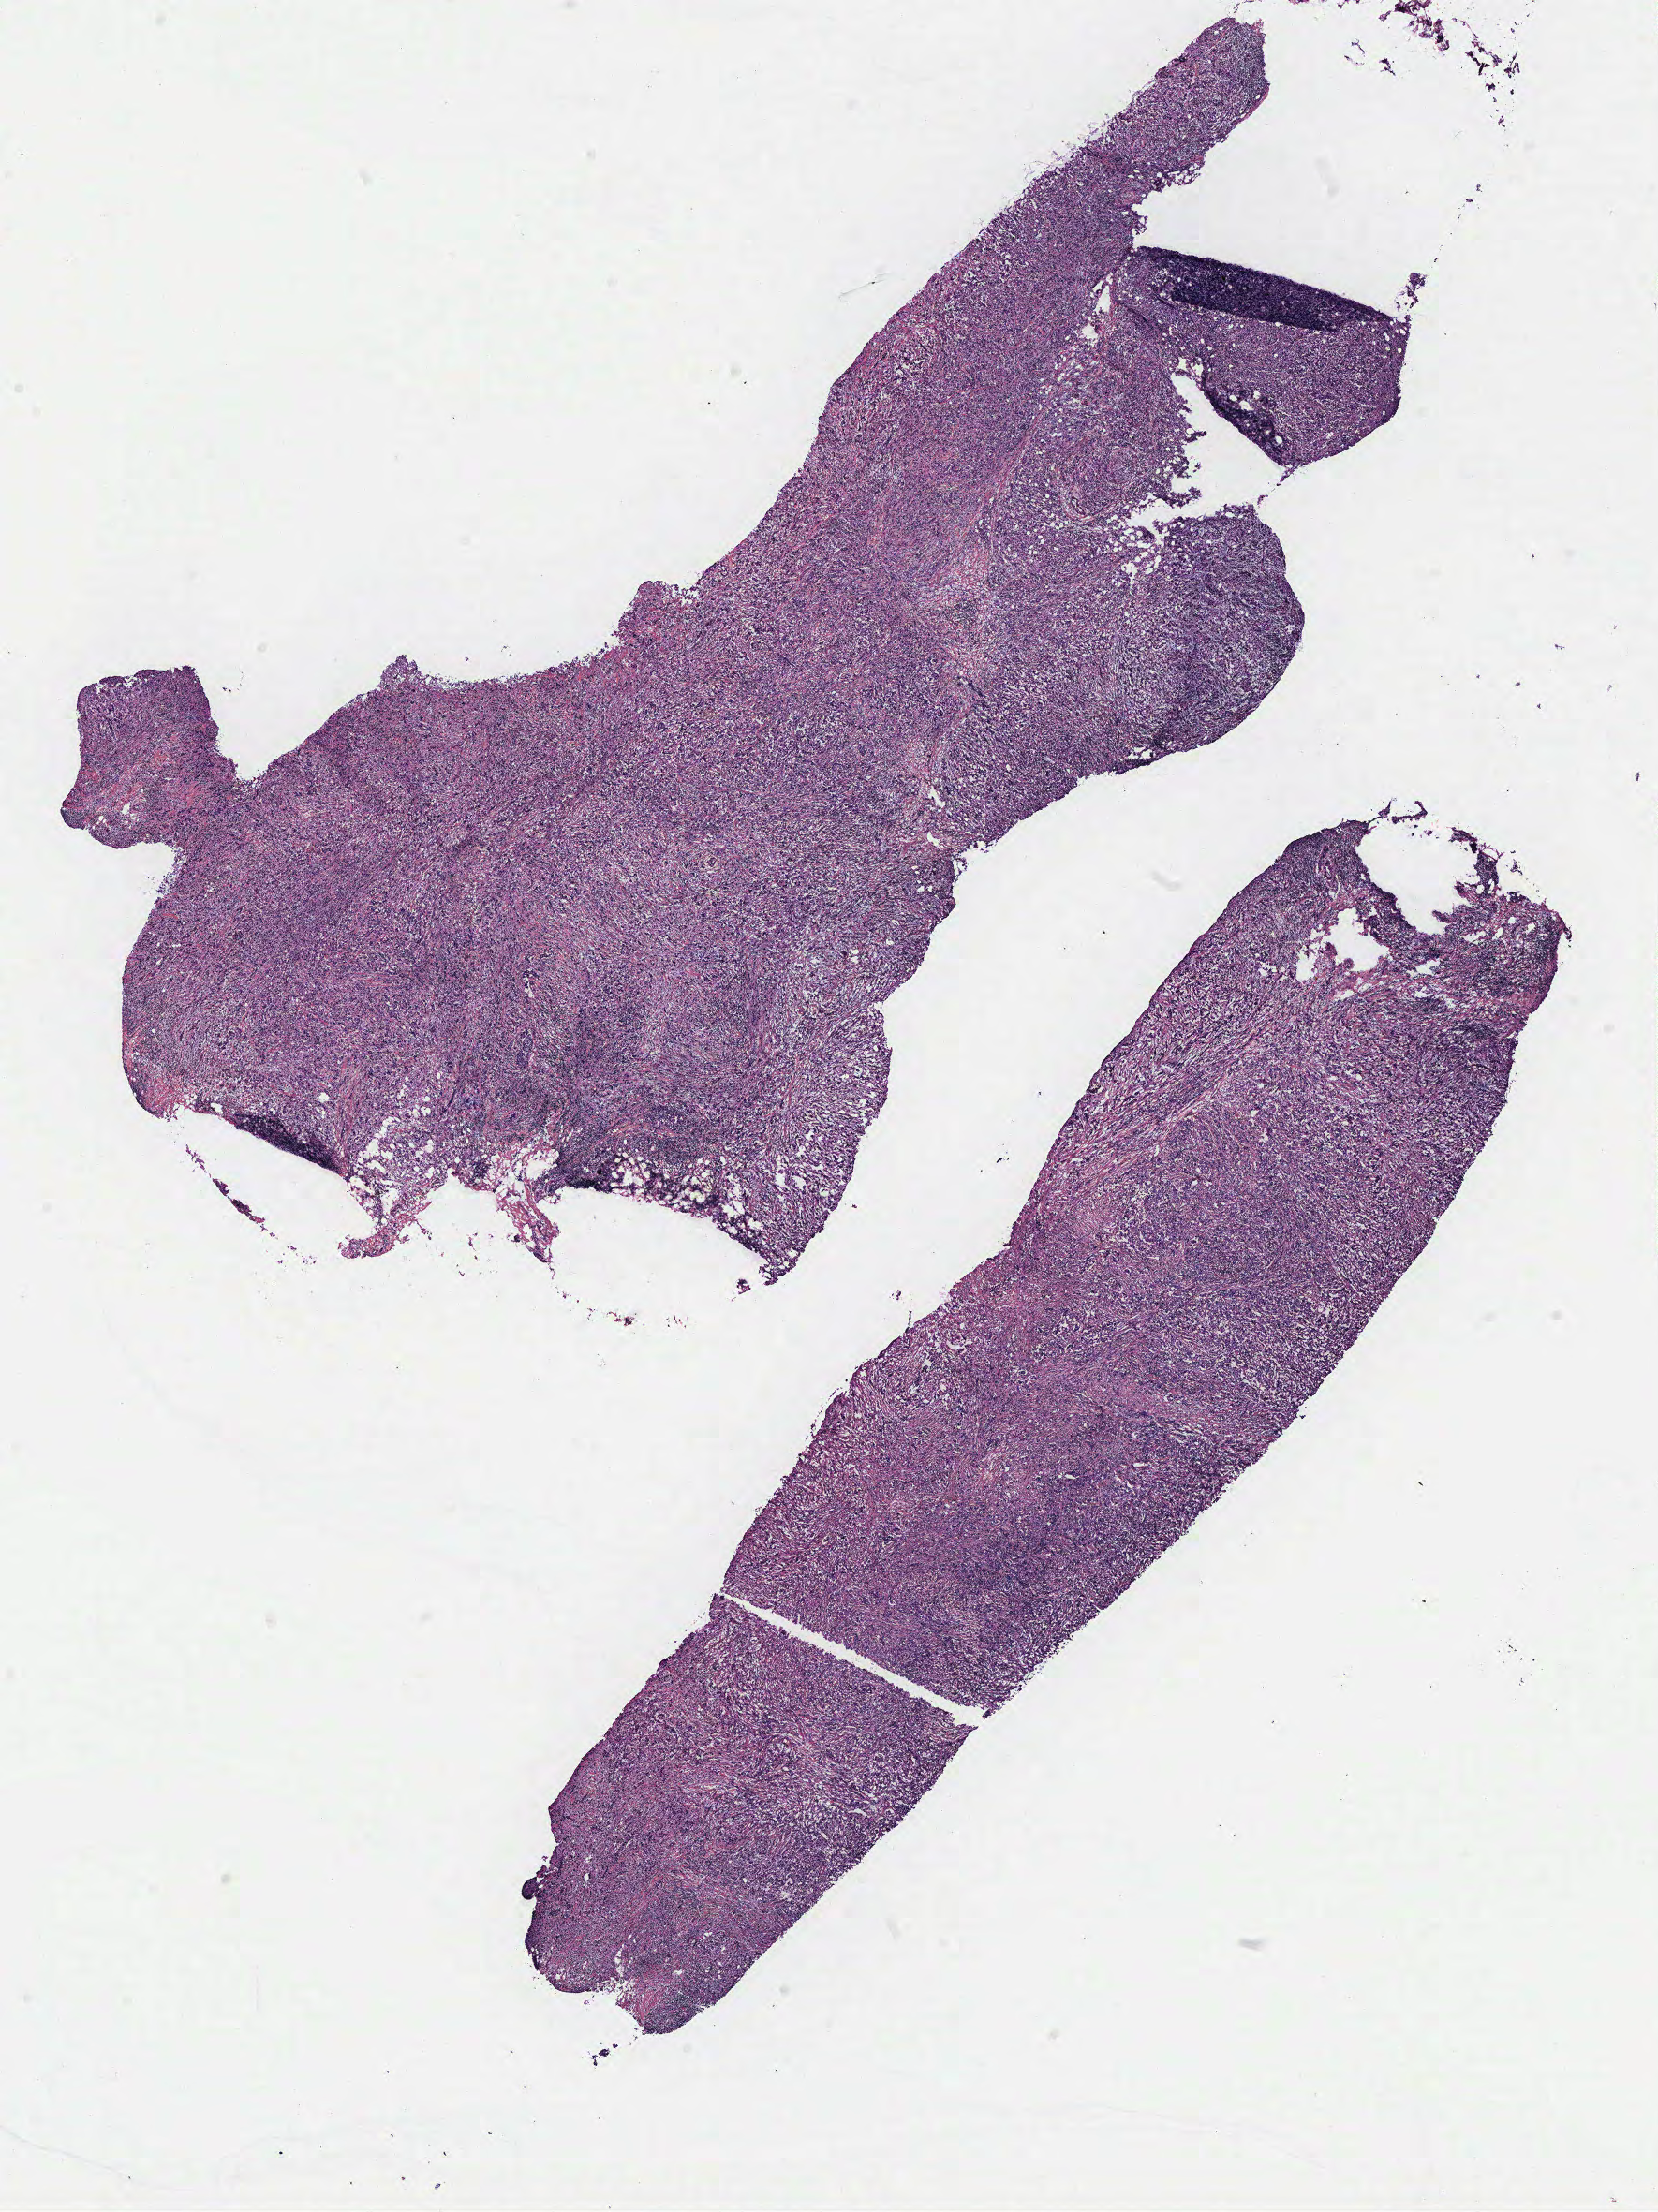
Digitized H&E-stained tissue section (whole slide), whole scanned area (about 14.2 x 18.9 mm, slide scanned at 40x) shown as a low-resolution overview. Breast, tissue type not recorded. 69-year-old female patient.
• patient diagnosis: Infiltrating duct carcinoma, NOS